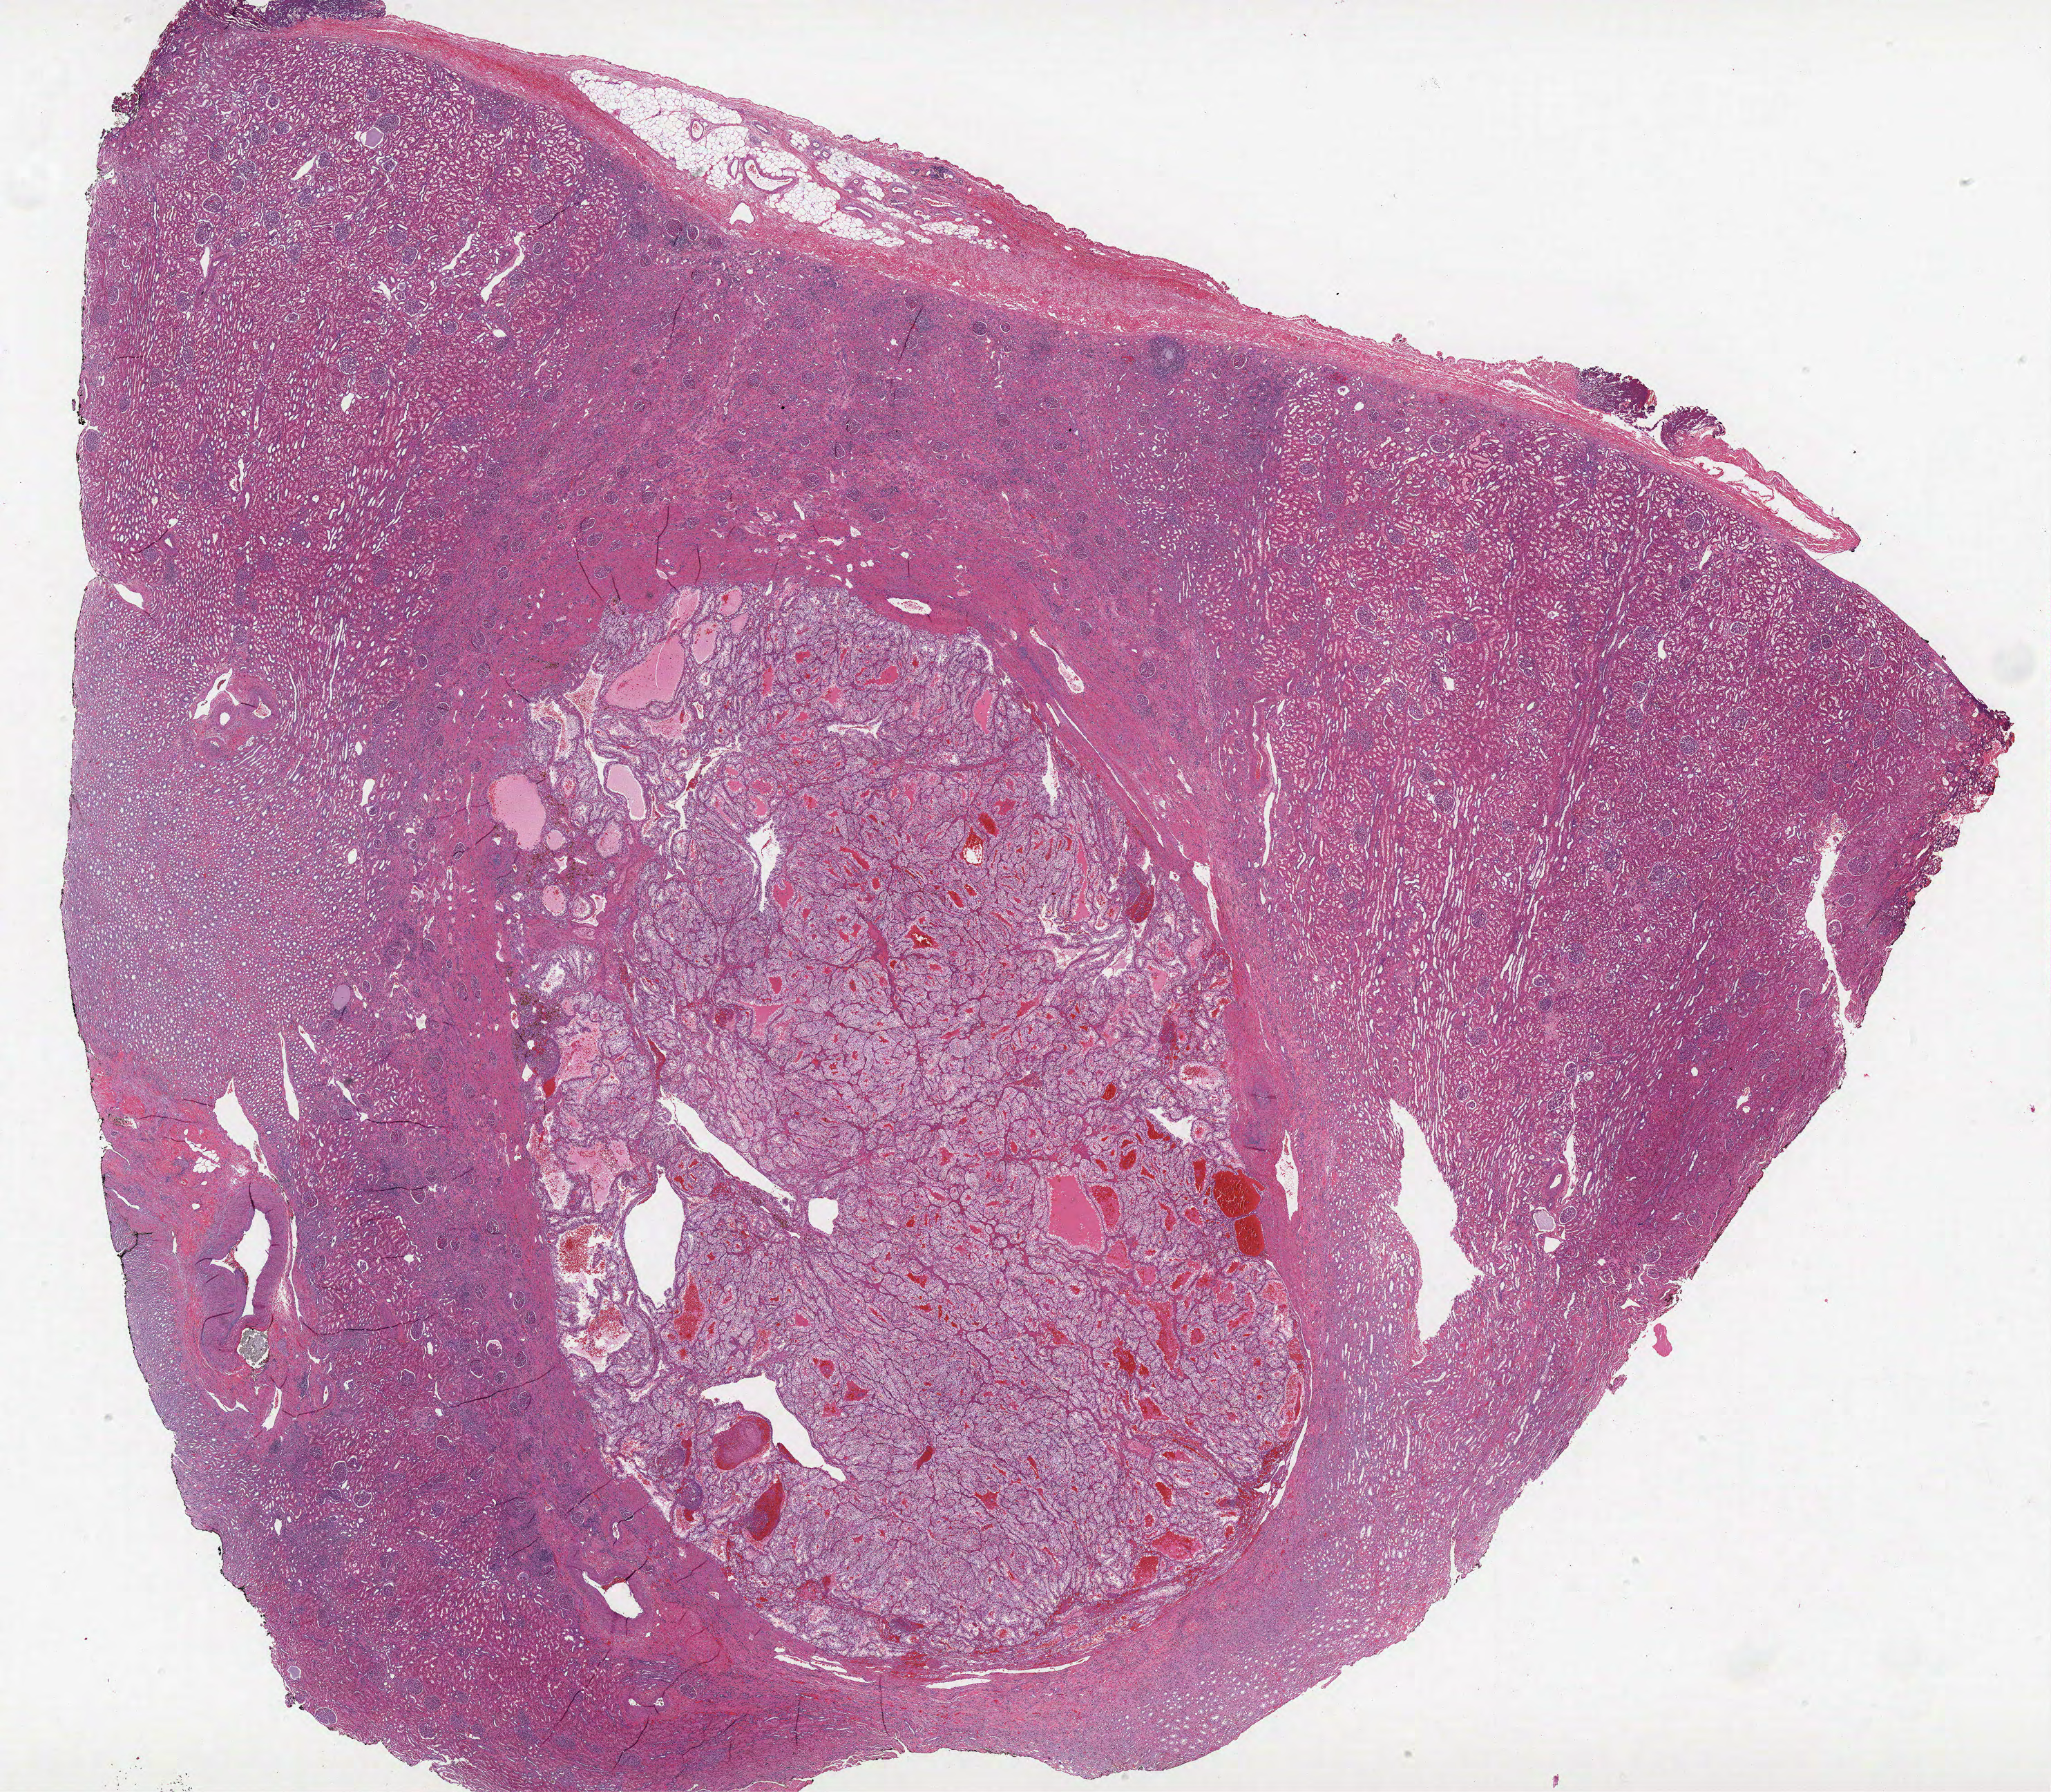
Whole-slide histology image, H&E-stained, a low-resolution overview of the entire scanned area, about 23.7 x 20.7 mm. Formalin-fixed paraffin-embedded (FFPE) diagnostic section. Kidney, primary tumour sample. Male patient; age at initial diagnosis 42 years. Histologic grade: G3 (poorly differentiated).
- diagnosis: Clear cell adenocarcinoma, NOS
- AJCC pathologic stage: I